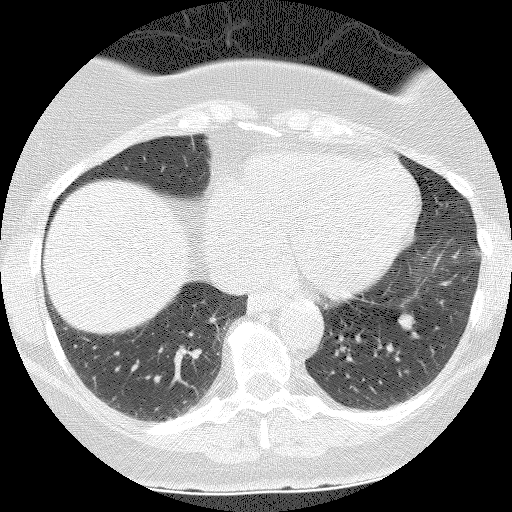
Axial slice from a low-dose chest CT screening exam. Second annual screen. Lung window (W 1500 / L -600 HU). 2.5 mm slice thickness. Slice 94 of 140 in the series. 512 × 512 image matrix, field of view 300 × 300 mm. Female participant, aged 55 years at enrolment. Former smoker at enrolment.
Expert-annotated lung lesion, bounding box <382,305,428,347> (left, top, right, bottom; pixels). The screening reader recorded 3 non-calcified nodules or masses ≥4 mm on this exam (left lower lobe, right lower lobe, right lower lobe); which of them this box marks is not recorded. Official screen result: positive, no significant change: stable abnormalities potentially related to lung cancer, unchanged since the prior screening exam. Lung cancer was diagnosed 655 days after this screen (after the third annual screen): carcinoid tumor, NOS, left lower lobe, carcinoid, stage not assessed, 10 mm at pathology.